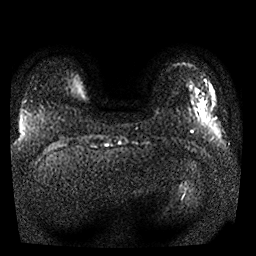
Breast MRI, one axial slice. Position 2 of 25 along the scan axis. Diffusion-weighted series; image 2 of 4 stored at this slice position (different b-values; order by instance number). 1.5 T. 256 × 256 image matrix, field of view 330 × 330 mm. Female patient.
Outlined on this slice (expert manual segmentation):
- tumour on diffusion-weighted imaging: box from (x=201, y=102) to (x=204, y=107) px